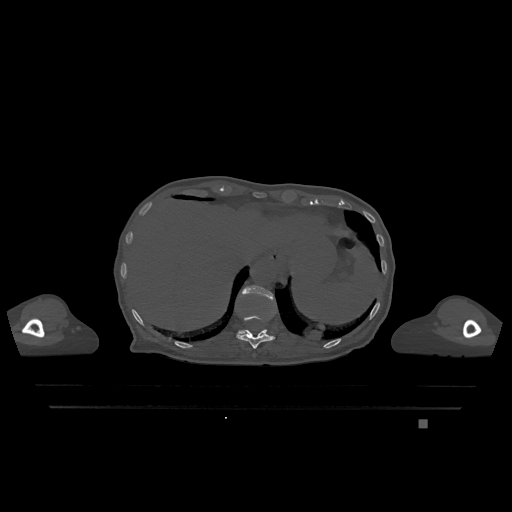
CT including the spine, one axial slice; slice 574 of 1317 in the series (ordered by position); bone window (W 1800 / L 400 HU); 0.5 mm slice thickness; 512 × 512 image matrix, field of view 500 × 500 mm. Patient: female, 74 years. Case-level facts recorded for this patient, not image findings: primary cancer: lung; vertebrae with lytic lesions (as recorded): T1, T4, T5, T6, L4, L5.
Outlined on this slice (semi-automatically segmented with operator editing):
- T11 vertebra: bounding box <236,315,275,349> (left, top, right, bottom; pixels)
- T12 vertebra: <238,285,275,334>